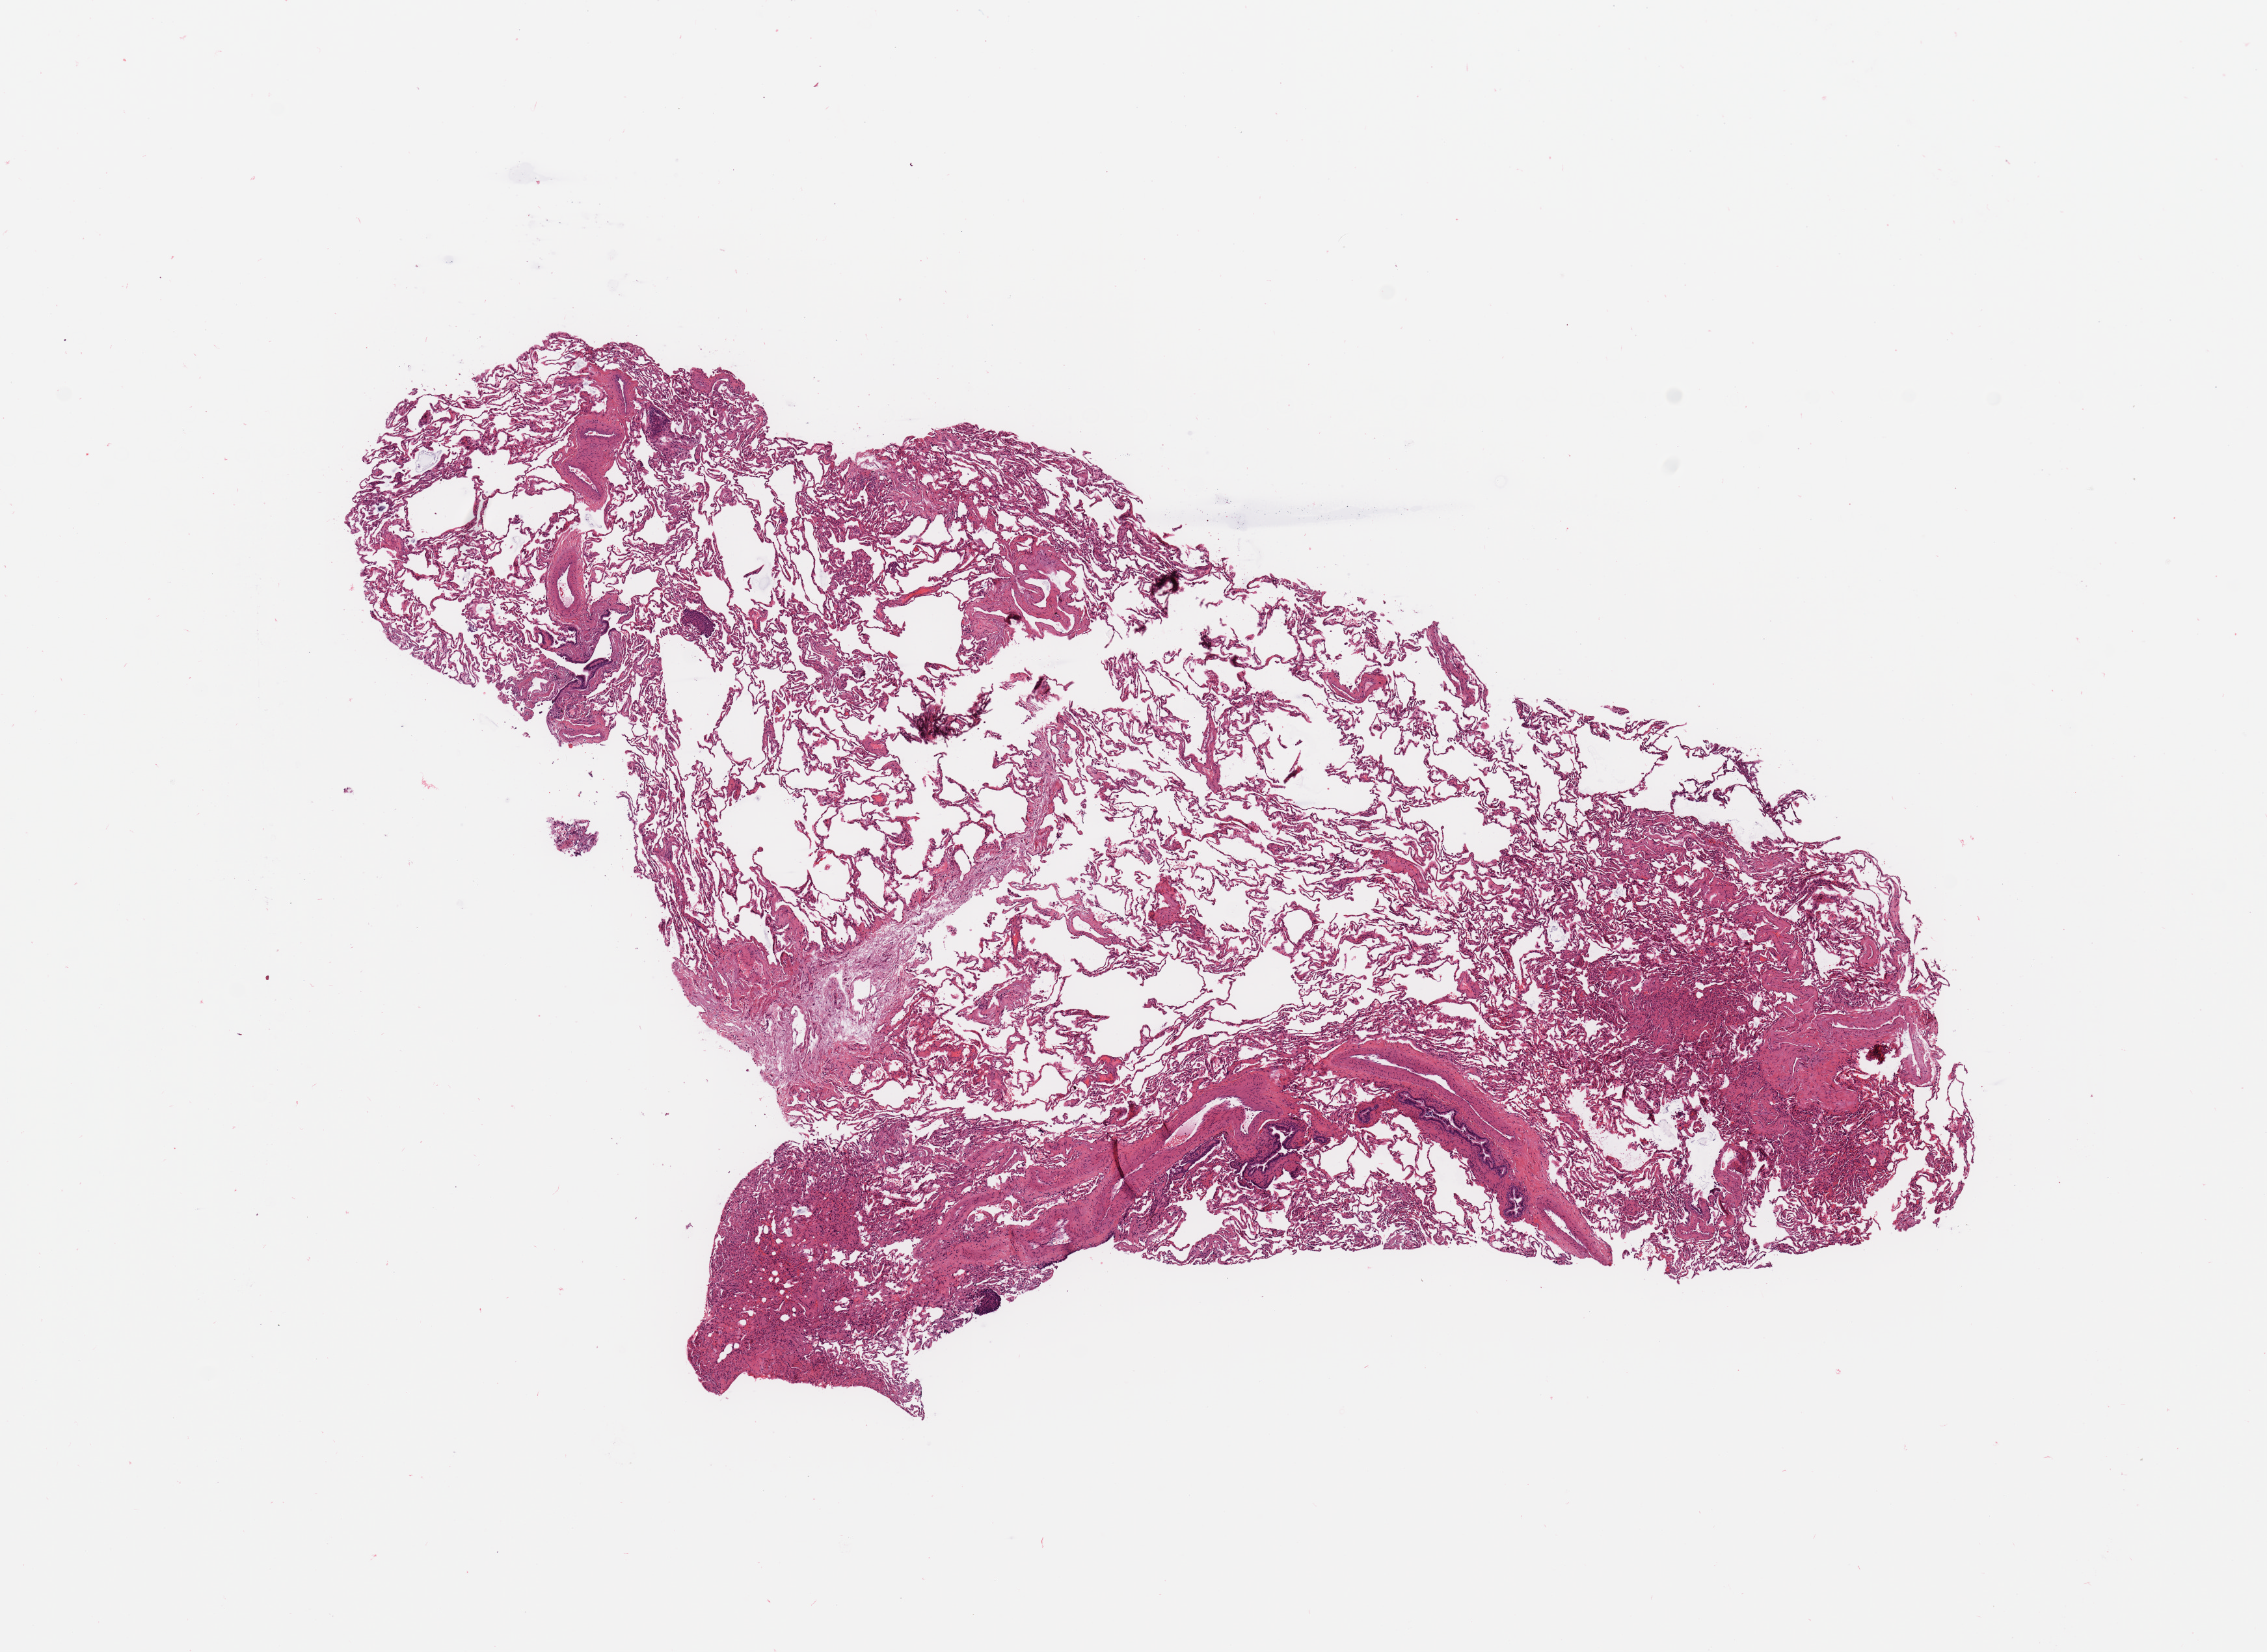
Hematoxylin and eosin (H&E) stained whole-slide image, a low-resolution overview of the entire scanned area, about 13.8 x 10.0 mm (slide scanned at 20x). Normal (non-tumour) tissue sample, sampled site: lung. Male, 67 y/o.
This section: normal (non-tumour) tissue from the same patient. Patient diagnosis: Squamous cell carcinoma, NOS.